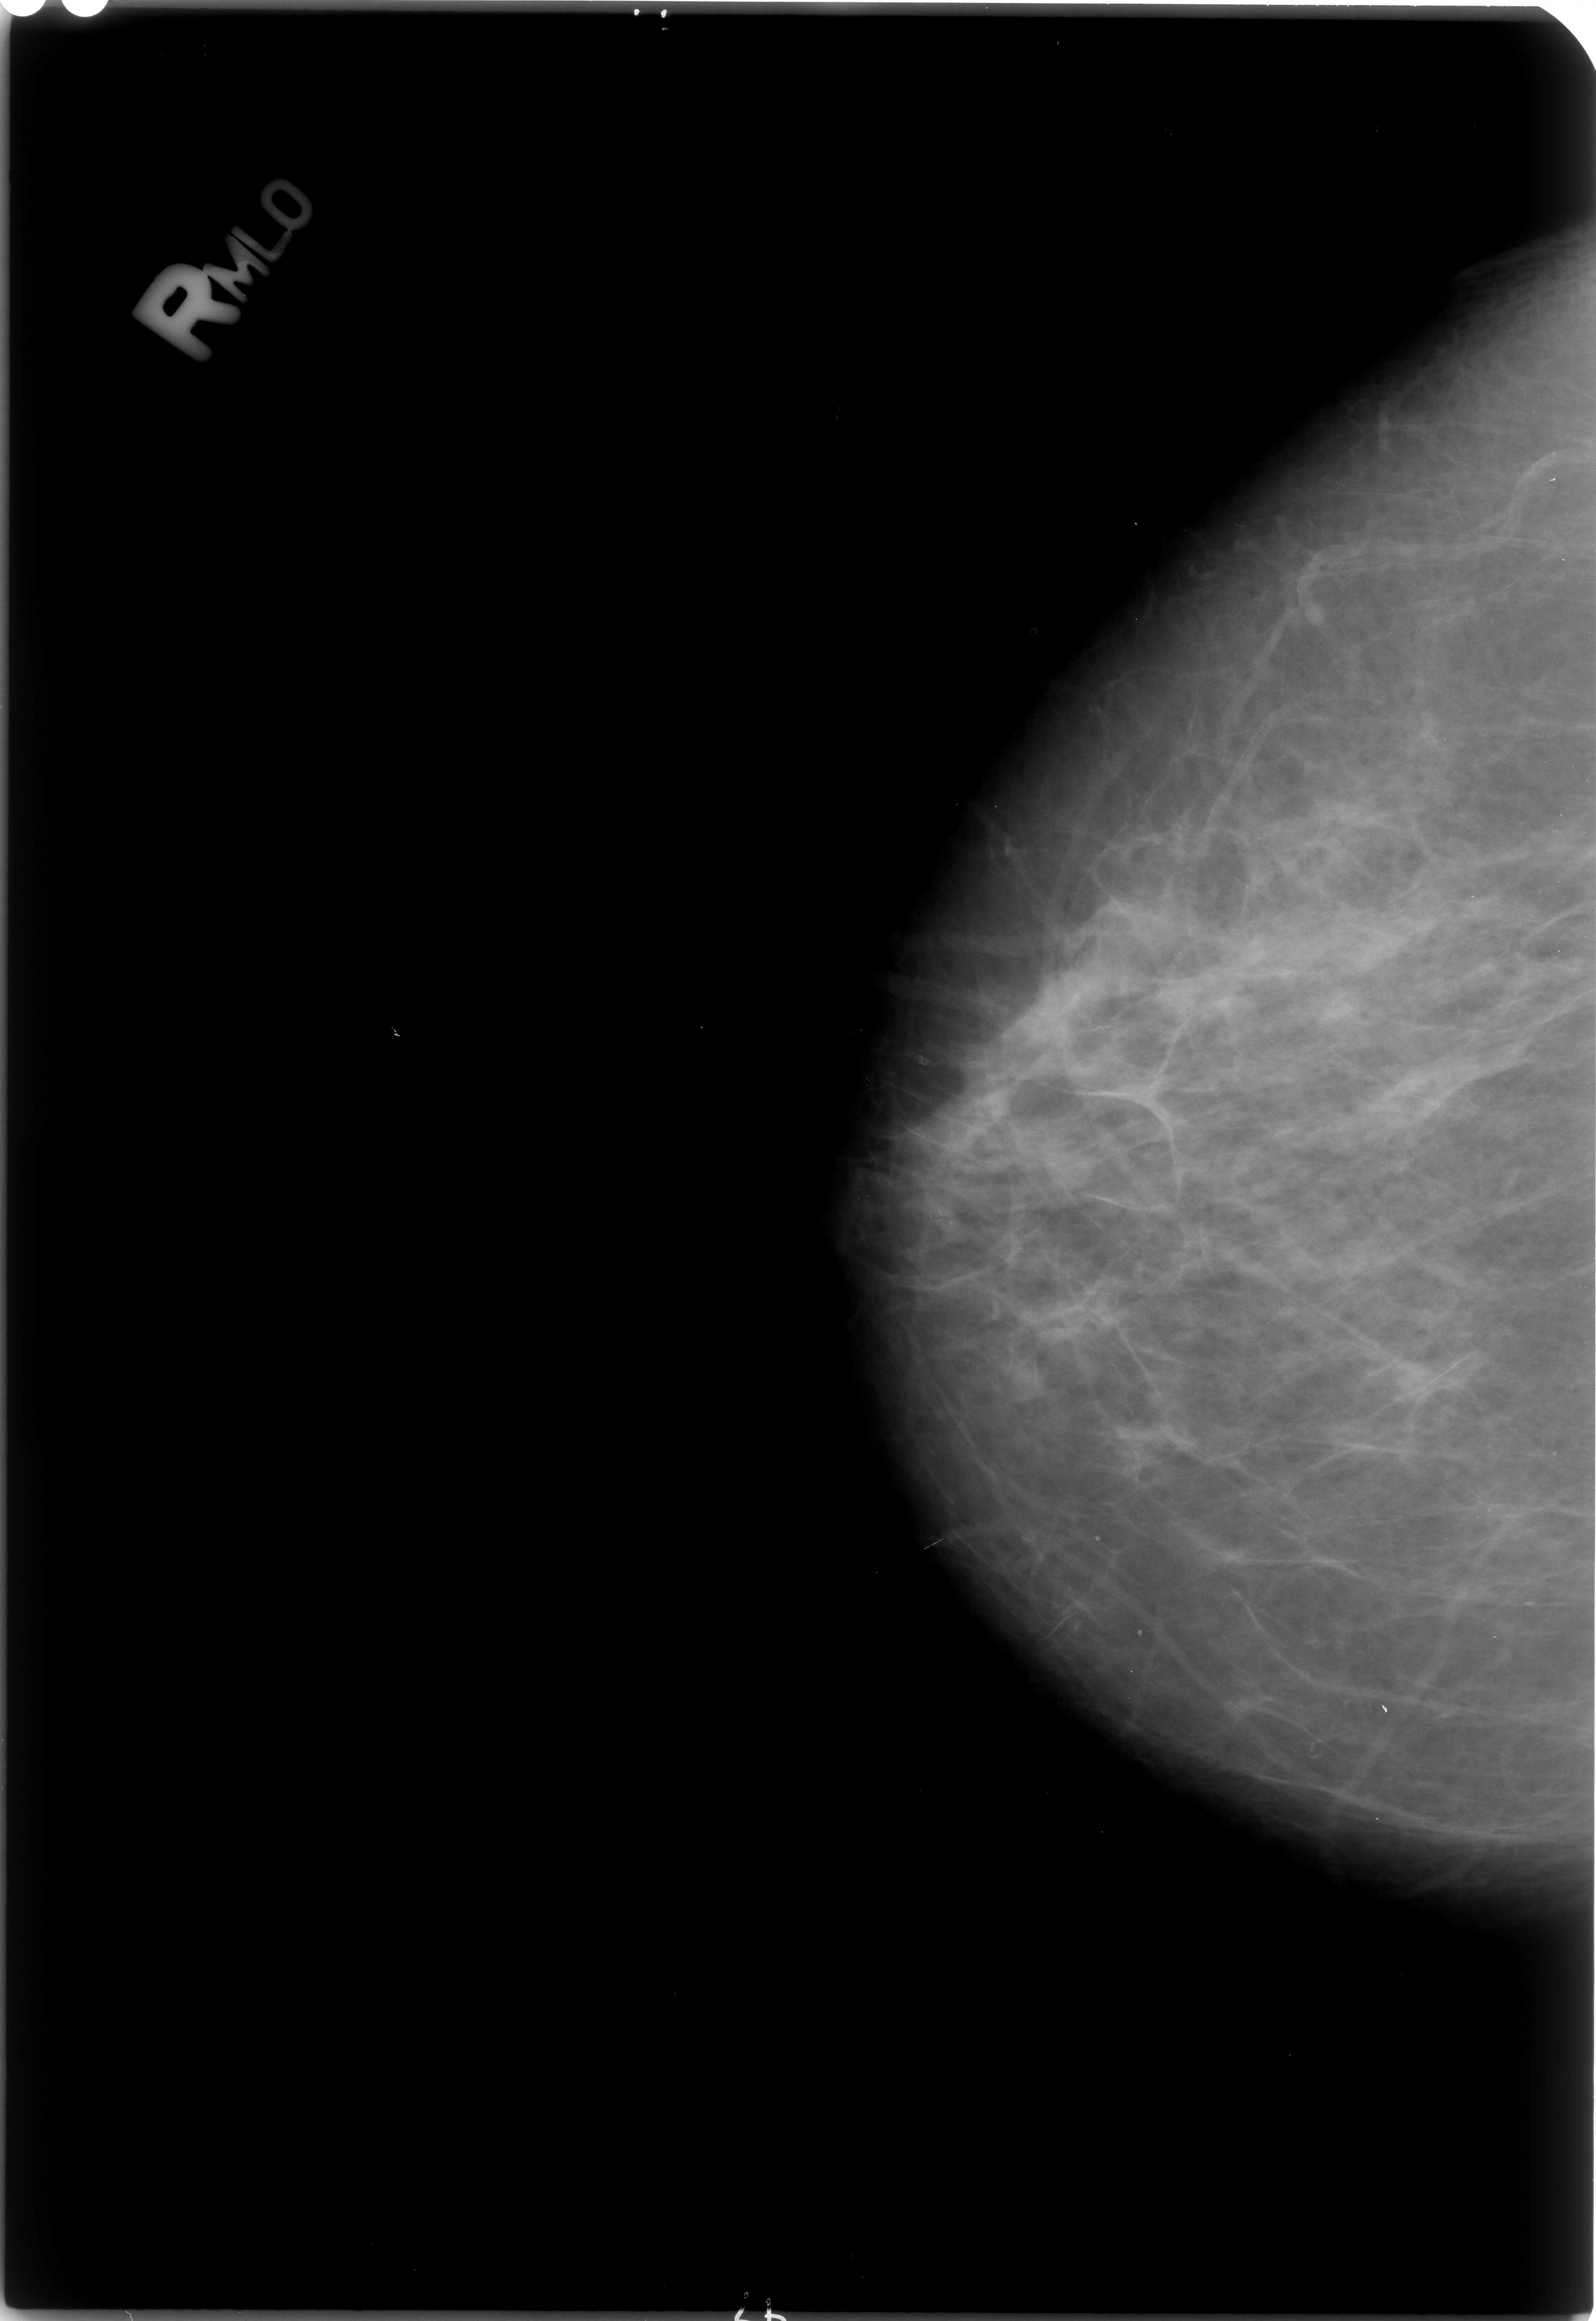
Scanned film-screen mammogram, right breast, craniocaudal (CC) view.
Abnormality record for this image: calcifications, morphology pleomorphic, distribution clustered; BI-RADS assessment category 4; pathology (as recorded): benign.